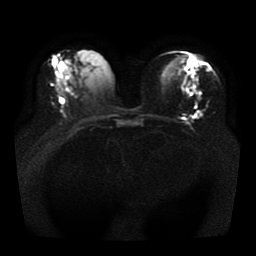
Breast MRI, one axial slice. Slice 16 of 41 in the series (ordered by position). Diffusion-weighted series; image 2 of 4 stored at this slice position (different b-values; order by instance number). 1.5 T. 5 mm slice thickness. 256 × 256 image matrix. Female patient.
Structures marked on this image (manually delineated by an expert):
- tumour on diffusion-weighted imaging: bounding box (x1, y1, x2, y2) in pixels: (195, 111, 202, 119)